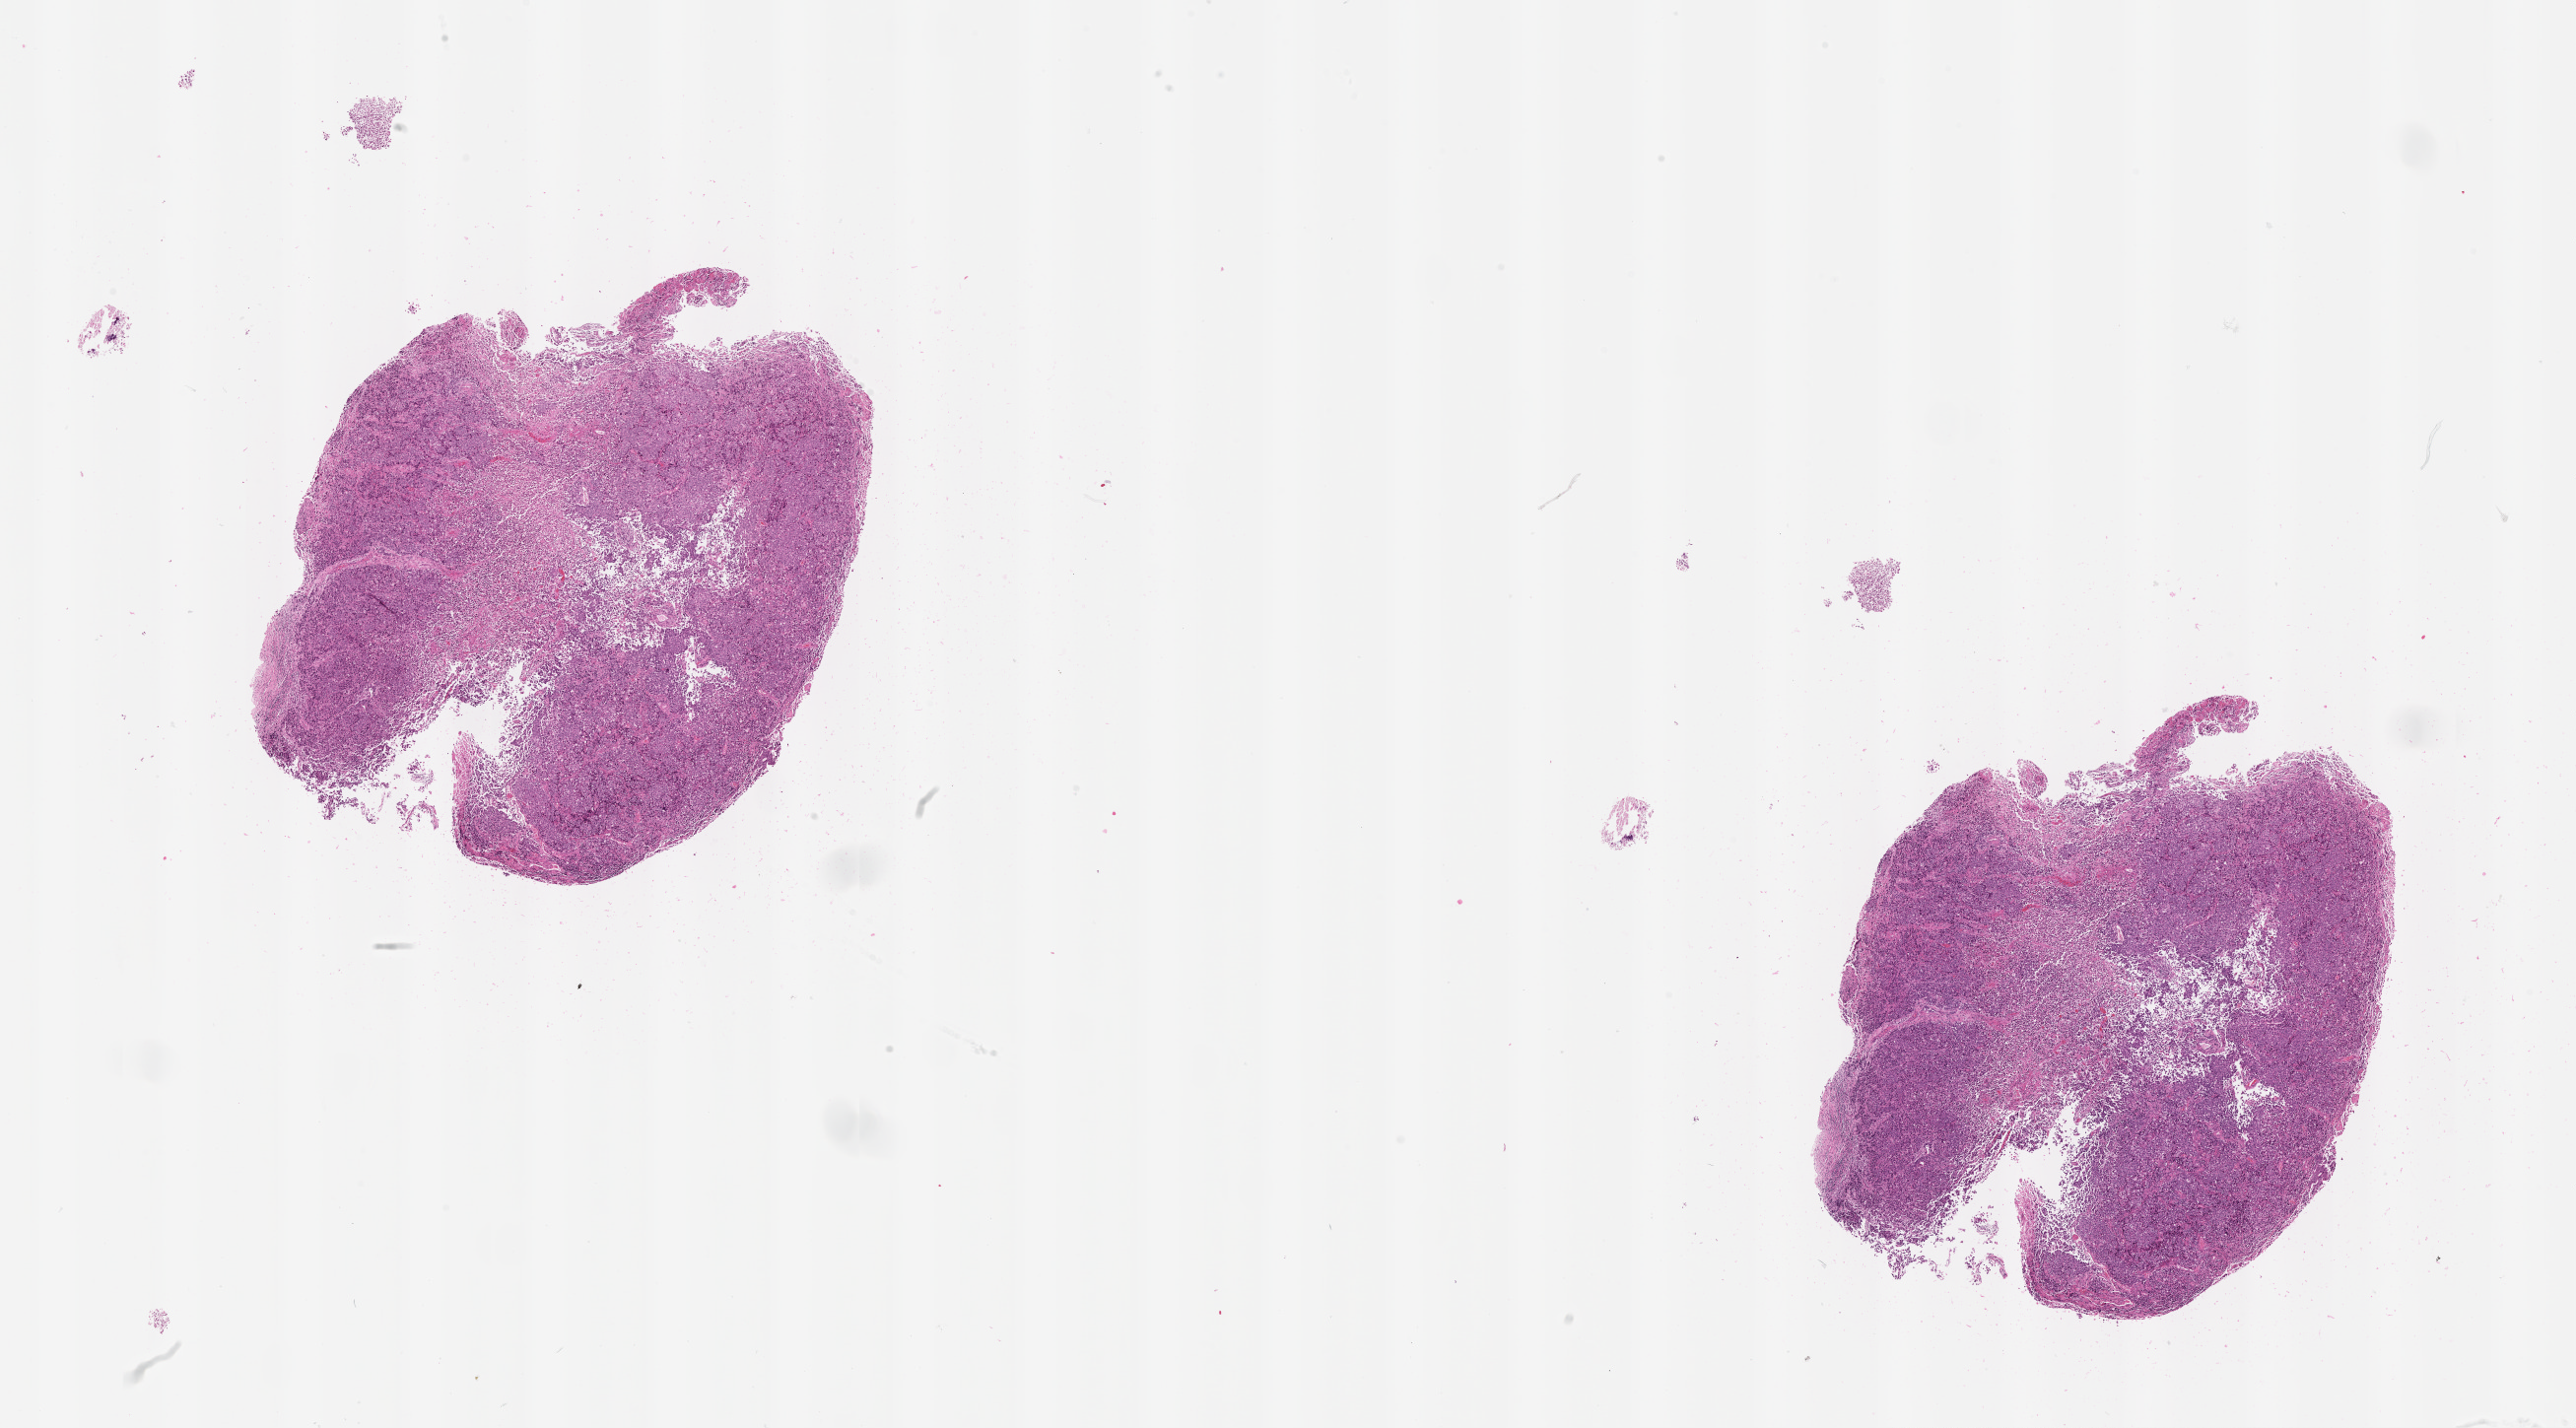
Whole-slide histology image, Hematoxylin and eosin (H&E) stained — a low-resolution overview of the entire scanned area, about 21.0 x 11.7 mm (slide scanned at 20x). Tumour tissue sample, sampled site: uterus. Female, 64 y/o. Histologic grade: G3 (poorly differentiated). Pathologist review of this section (percent, as recorded): tumour nuclei 80%, necrosis 0%.
Histologic diagnosis: Endometrioid adenocarcinoma, NOS. AJCC pathologic stage: IIIC2.